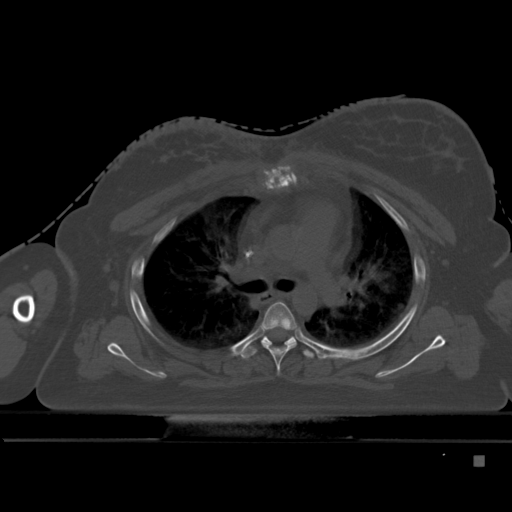
CT including the spine, one axial slice; position 327 of 495 along the scan axis; bone window (W 1800 / L 400 HU); 1.5 mm slice thickness; 512 × 512 image matrix, field of view 404 × 404 mm. Patient: female, 33 years. From the clinical record (not read from this slice): primary cancer: breast.
Annotated regions visible in this slice (semi-automatically segmented with operator editing):
- T4 vertebra: bounding box (x1, y1, x2, y2) in pixels: (262, 301, 297, 375)
- T5 vertebra: (241, 332, 314, 359)